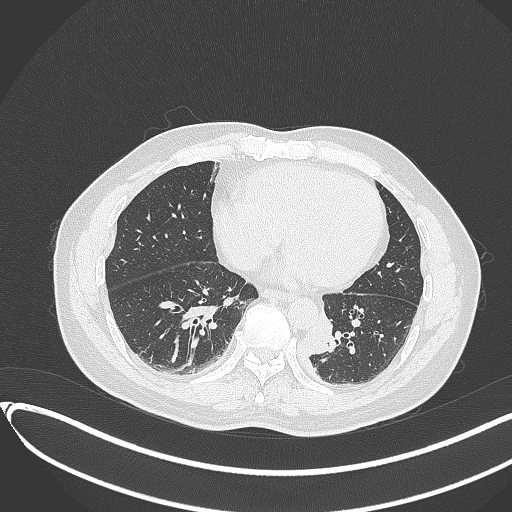
Chest CT, one axial slice; slice 116 of 417 in the series (ordered by position); 120 kVp; lung window (W 1500 / L -600 HU); 1 mm slice thickness; 512 × 512 image matrix. Patient: male, 54 years. From the clinical record (not read from this slice): clinical TNM (as recorded): T3 N0 M0.
Outlined on this slice (bounding box drawn by a radiologist):
- lung tumour (recorded histology: squamous cell carcinoma): bounding box <296,304,333,355> (left, top, right, bottom; pixels)